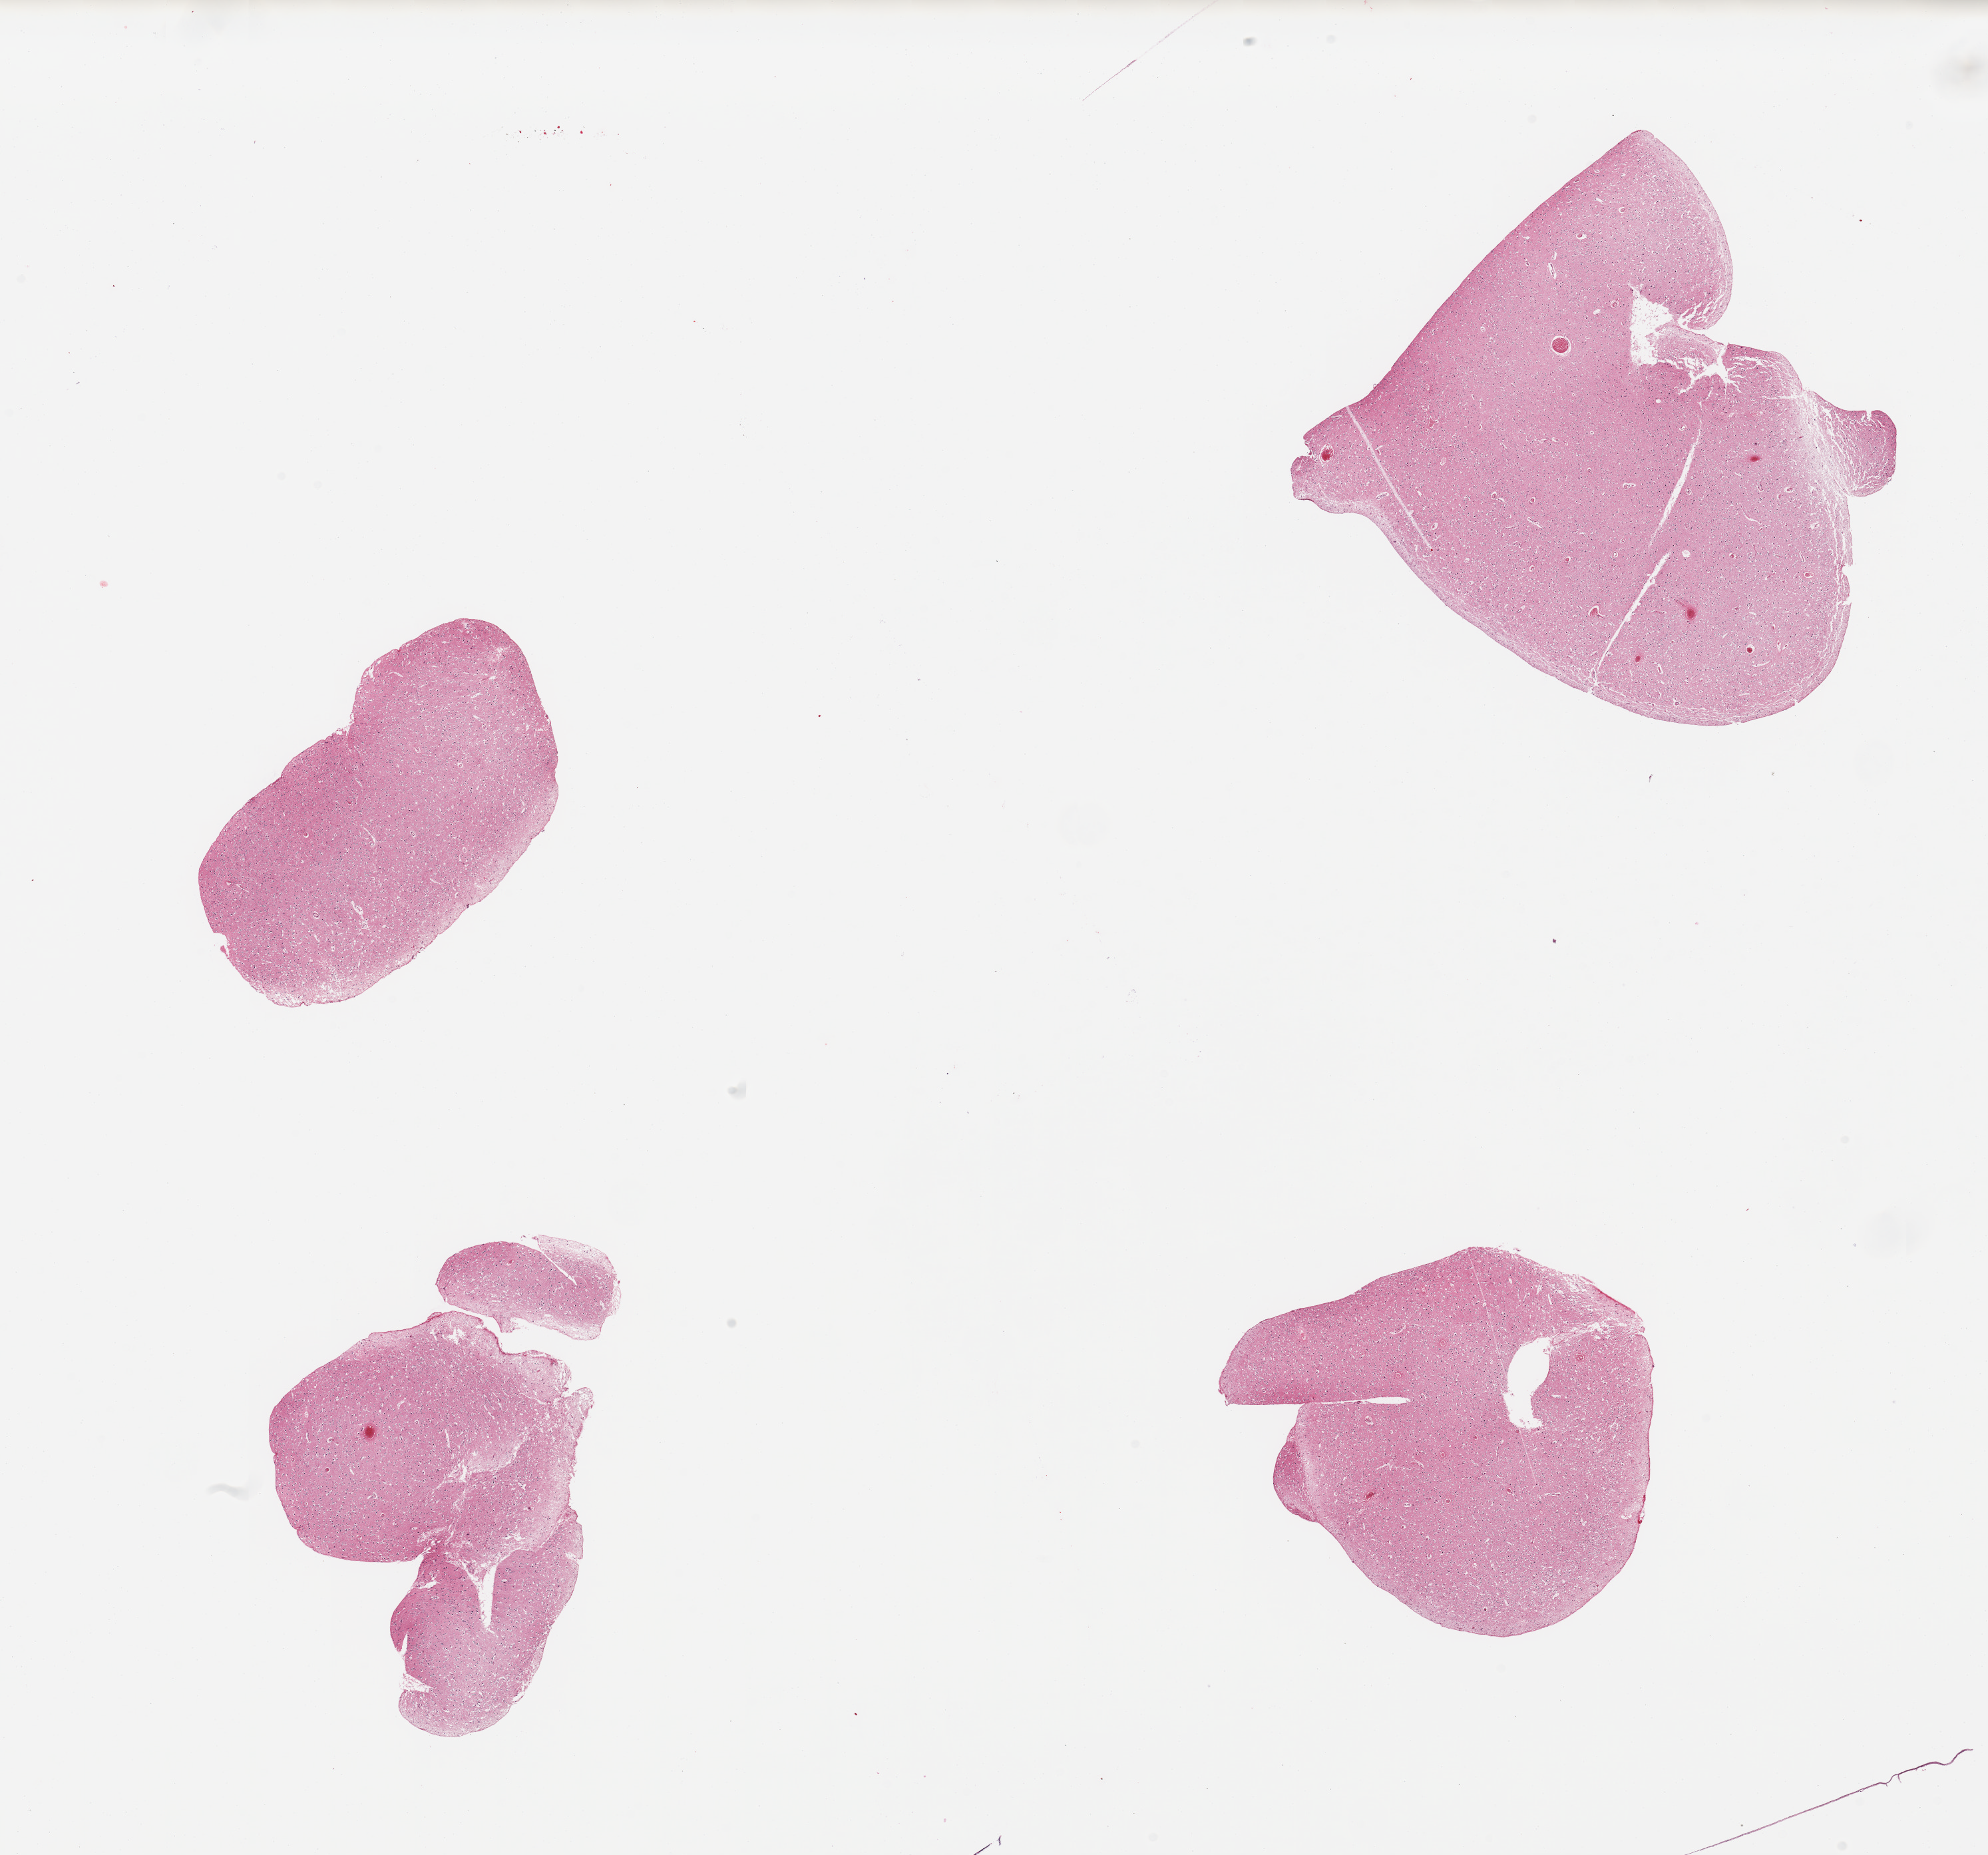
Haematoxylin and eosin whole-slide image, brightfield, shown as a low-resolution overview of the whole scanned area (about 23.6 x 22.0 mm), PAXgene-fixed, paraffin-embedded tissue, sampled site (target tissue): cerebral cortex, tissue donor sample. Male donor.
- pathologist's review note for this sample: 4pieces